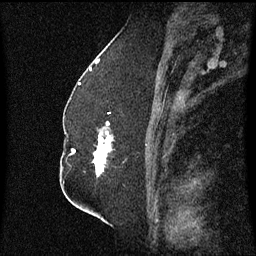
Breast MRI (dynamic contrast-enhanced), one sagittal slice. Slice 32 of 60 in the series (ordered by position). Dynamic contrast-enhanced series, image 2 of 3 at this slice position (ordered by acquisition). 1.5 T. TE 4.2 ms, TR 8.4 ms. 2.3 mm slice thickness. 256 × 256 image matrix, field of view 200 × 200 mm. Female patient, age 52 years. Case-level facts recorded for this patient, not image findings: setting: breast cancer imaged before/during neoadjuvant chemotherapy; receptor status: HR-positive, HER2-negative.
Outlined on this slice (semi-automatic segmentation, software-assisted and operator-edited):
- analysis volume of interest (the breast-tissue region the enhancement analysis was run in; not a lesion): bounding box (x1, y1, x2, y2) in pixels: (93, 114, 113, 177)
- tumour enhancement mask (voxels above the 70 % enhancement threshold inside the analysis volume of interest): (94, 122, 112, 175)